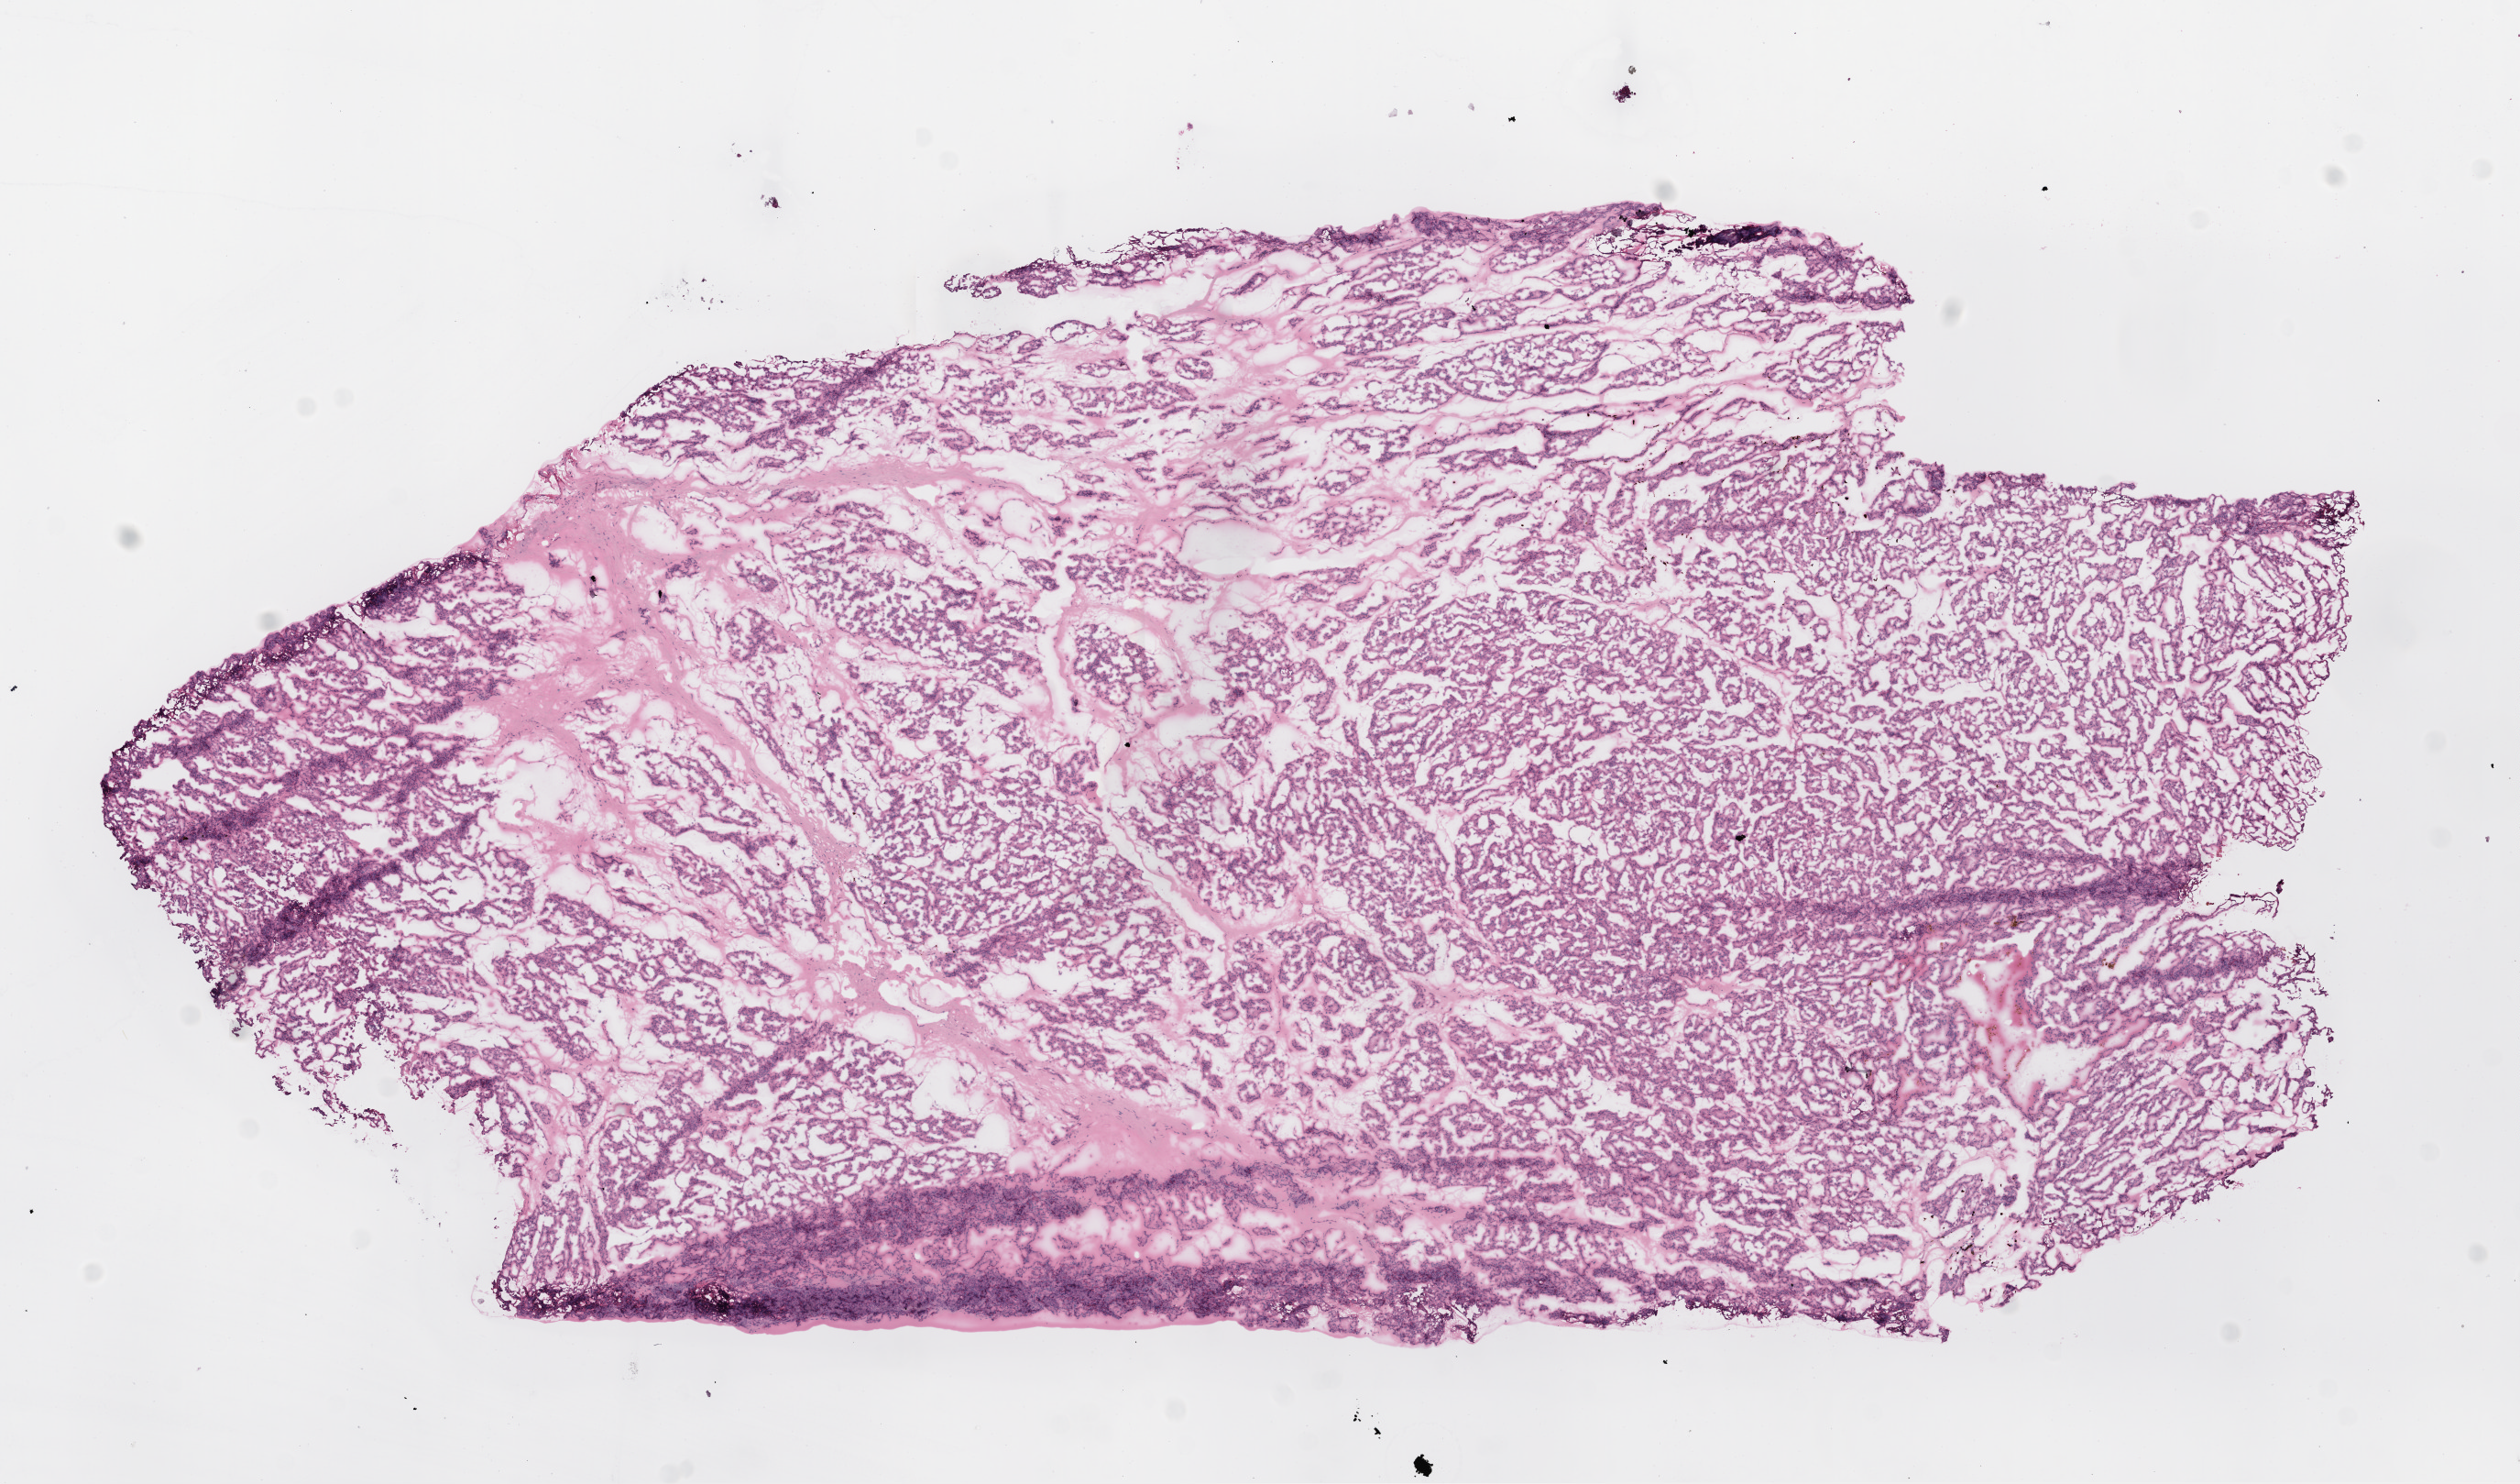
Whole-slide histology image, H&E — shown as a low-resolution overview of the whole scanned area (about 11.0 x 6.5 mm, from a 20x scan). Frozen section from the top of the tissue portion. Kidney, primary tumour sample. Male, age 45 years at initial diagnosis. Composition of this section per pathologist review: tumour cells 85%, tumour nuclei 85%.
Histologic diagnosis: Clear cell adenocarcinoma, NOS.